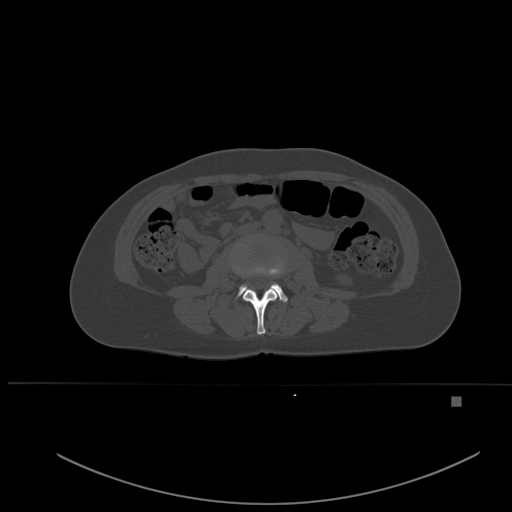
CT including the spine, one axial slice; position 204 of 651 along the scan axis; bone window (W 1800 / L 400 HU); 1.5 mm slice thickness; 512 × 512 image matrix, field of view 443 × 443 mm. Female patient, age 49 years. Case-level facts recorded for this patient, not image findings: primary cancer: breast; vertebrae with lytic lesions (as recorded): L3, T12, L4.
Structures marked on this image (semi-automatically segmented with operator editing):
- L2 vertebra: bounding box [x1, y1, x2, y2] px = [233, 257, 284, 335]
- L3 vertebra: [238, 265, 288, 302]